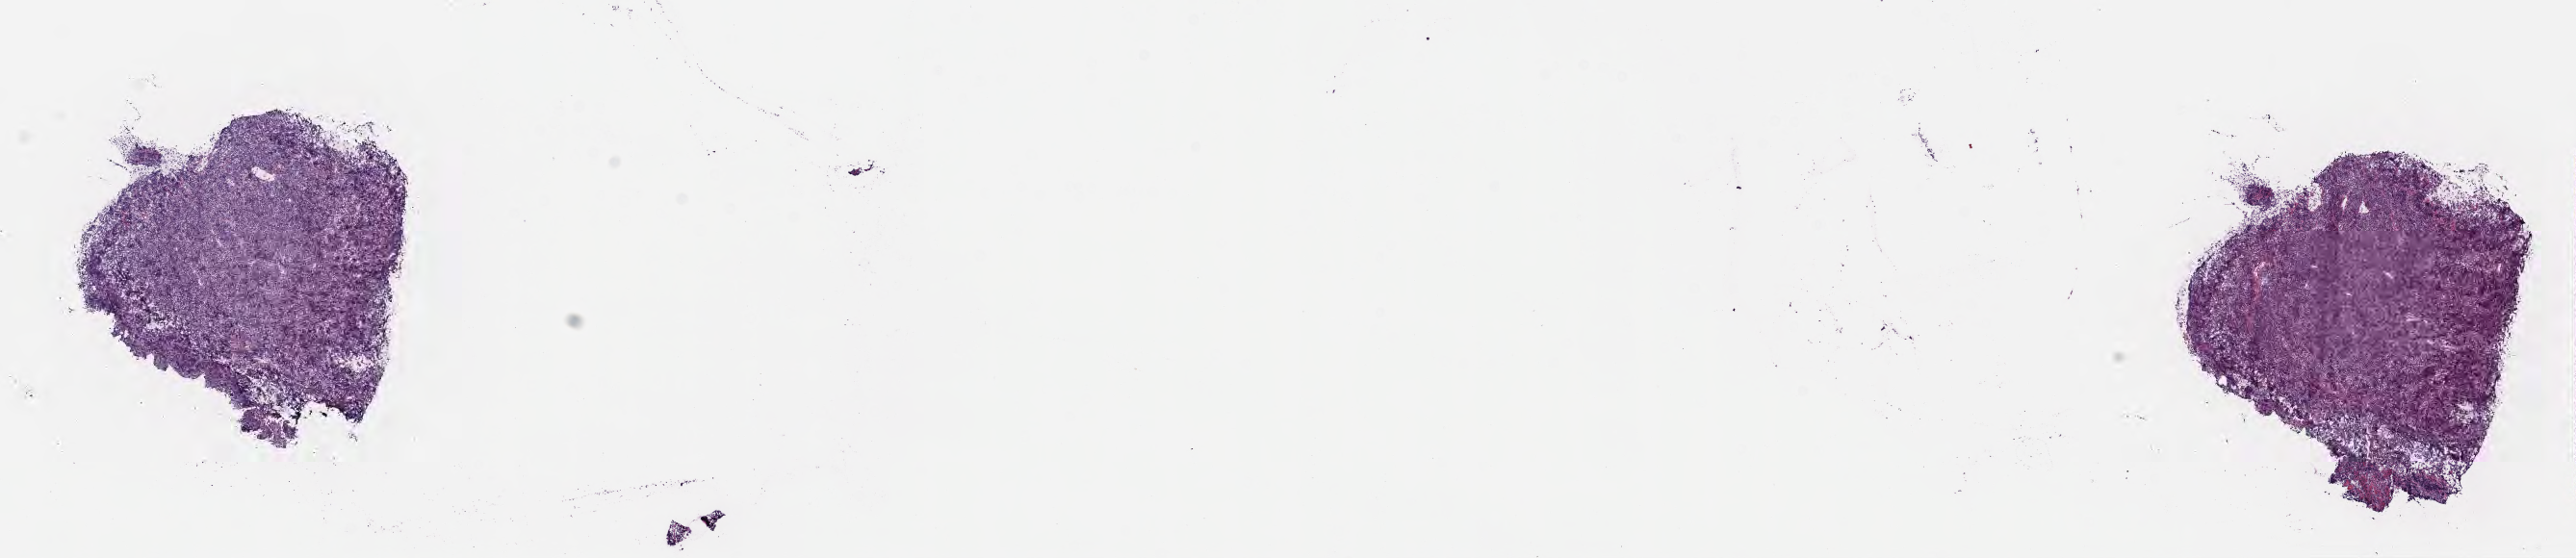
Whole-slide image, haematoxylin and eosin stain, shown as a low-resolution overview of the whole scanned area (about 21.6 x 4.7 mm), frozen section, specimen: primary tumor, anatomic site: cranium. Female patient; age at initial diagnosis 7 years. Slide review estimates, as recorded: tumor cells 90%, tumor nuclei 95%, stromal cells 5%, necrosis 5%, normal cells 0%. Inflammatory infiltration, as recorded: lymphocyte infiltration 70%, monocyte infiltration 15%, neutrophil infiltration 0%.
- Ann Arbor stage (patient): Stage IV
- diagnosis: Burkitt lymphoma, NOS